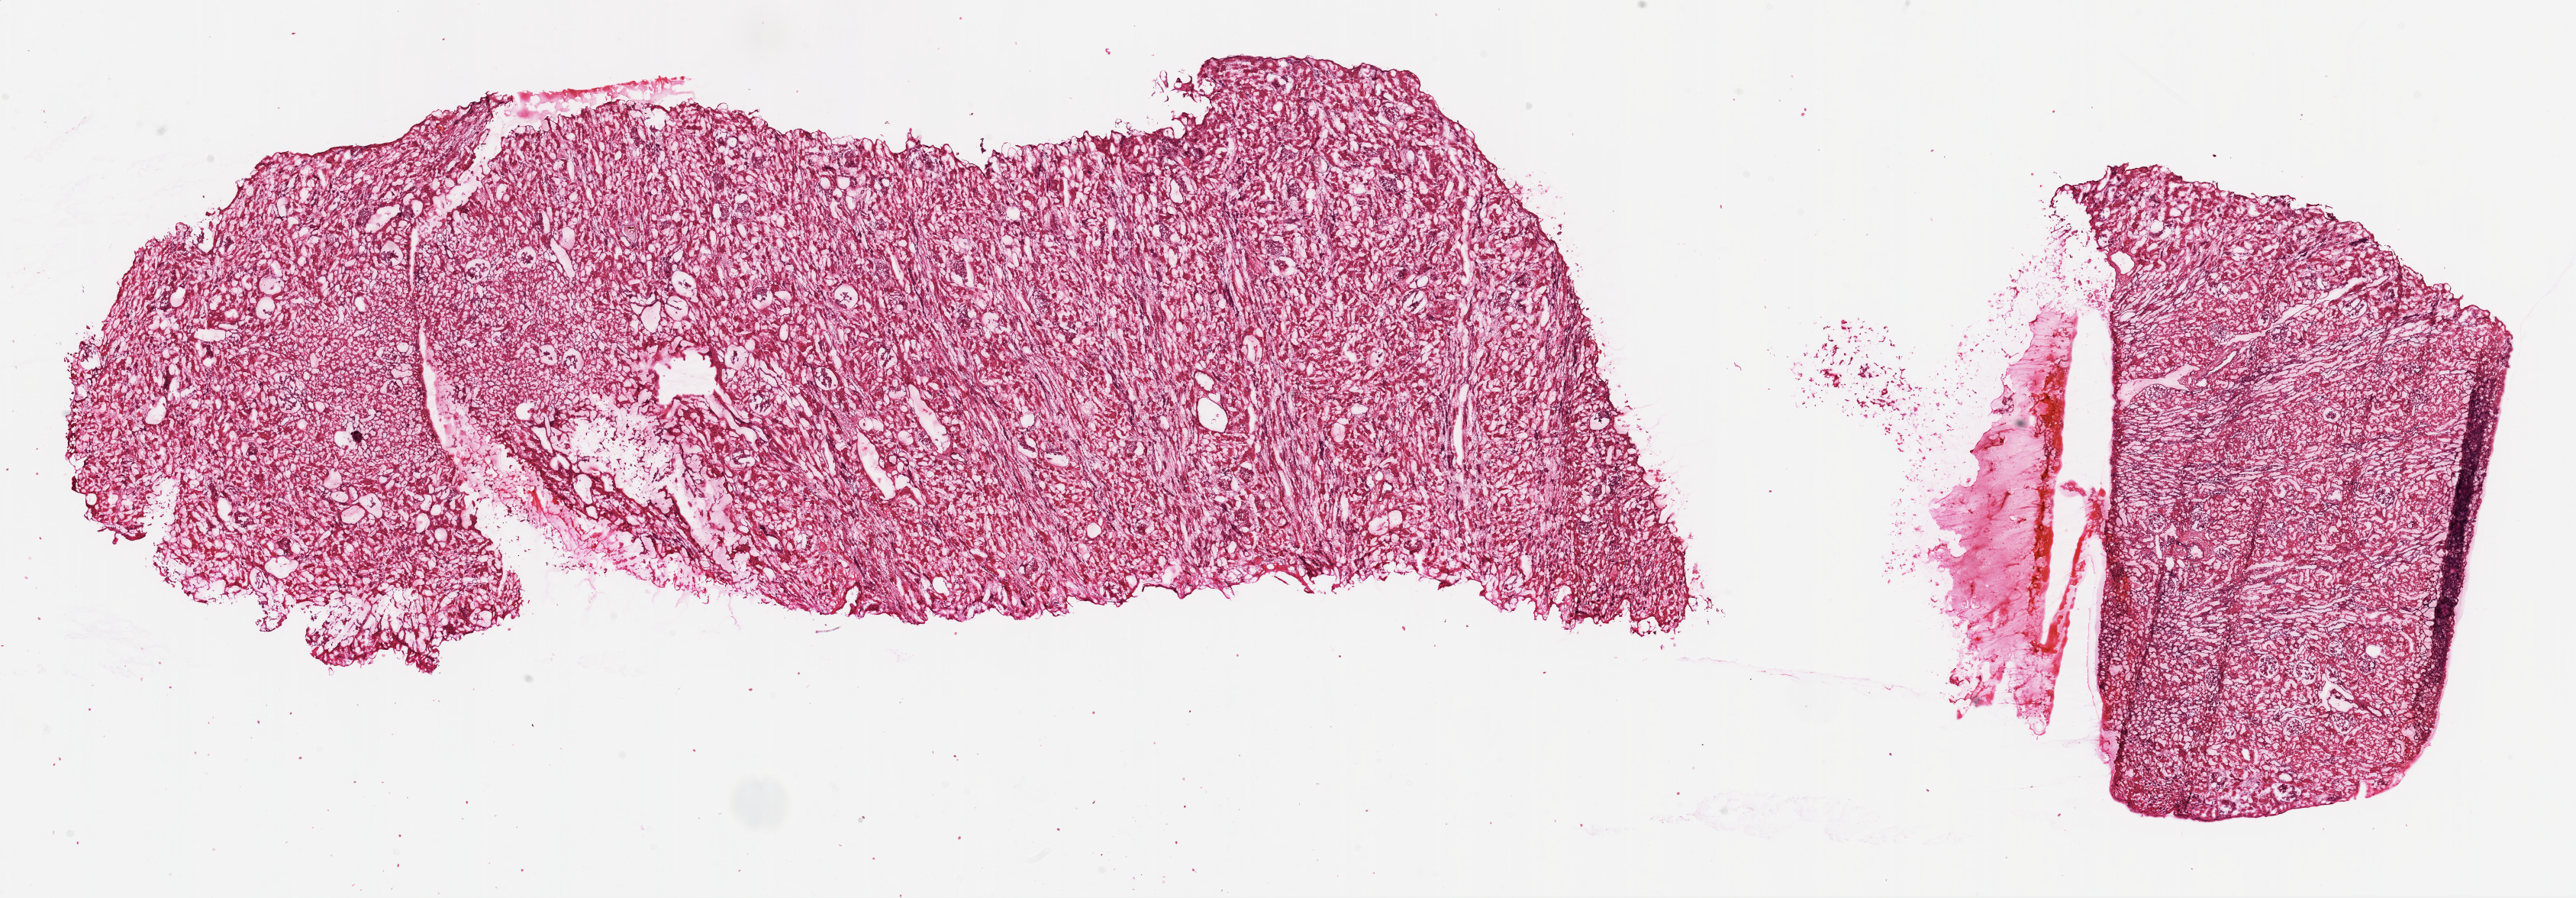
H&E-stained whole-slide image, shown as a low-resolution overview of the whole scanned area (about 27.1 x 9.4 mm), frozen section from the top of the tissue portion, solid tissue normal (non-tumour tissue) sample from the kidney. Male, age 47 years at initial diagnosis.
* this section: solid tissue normal sample (biorepository sample class)
* patient diagnosis: Clear cell adenocarcinoma, NOS